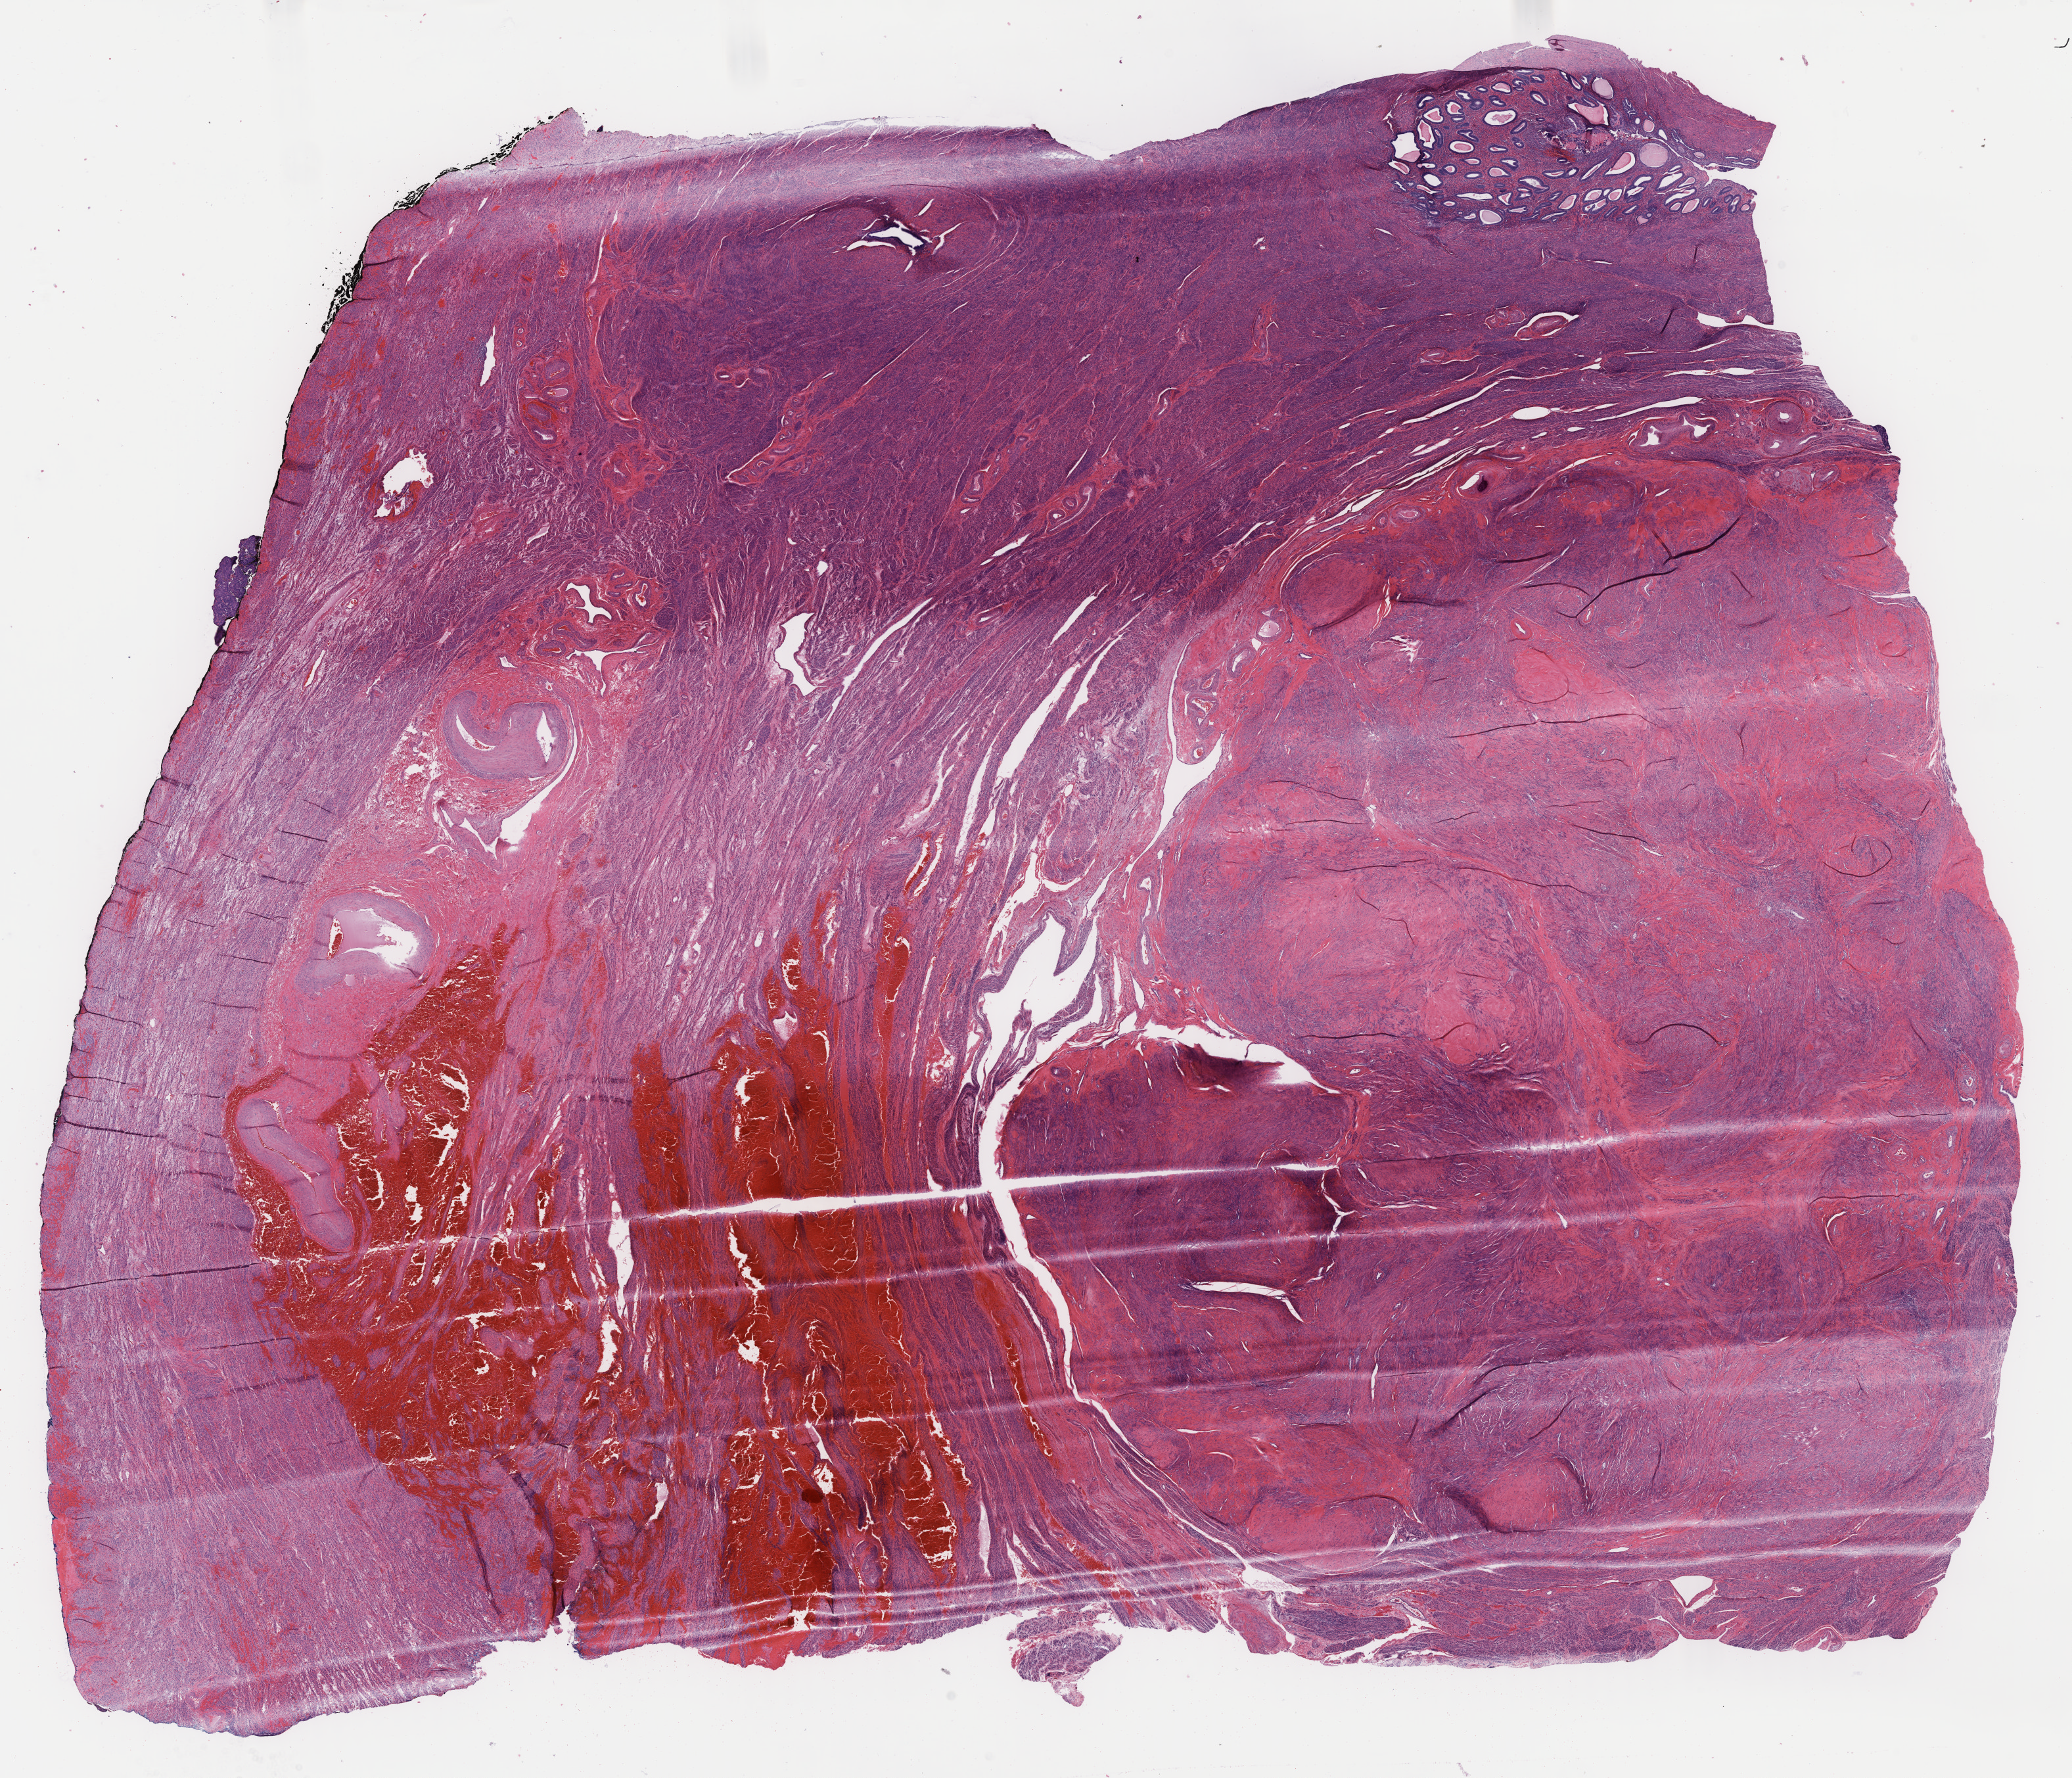
H&E whole-slide image, a low-resolution overview of the entire scanned area, about 25.0 x 21.4 mm, frozen section, specimen: non-tumor (normal tissue) sample from a patient with adenocarcinoma with mixed subtypes, anatomic site: endometrium. Patient sex: female. Slide review estimates, as recorded: tumor cells 0%, tumor nuclei 0%, stromal cells 100%, necrosis 0%, normal cells 0%. Infiltration values recorded for this section: lymphocyte infiltration 6%, monocyte infiltration 2%, neutrophil infiltration 7%.
This section: non-tumor tissue sample; the patient's diagnosis is given above. Section: top of the tissue portion.